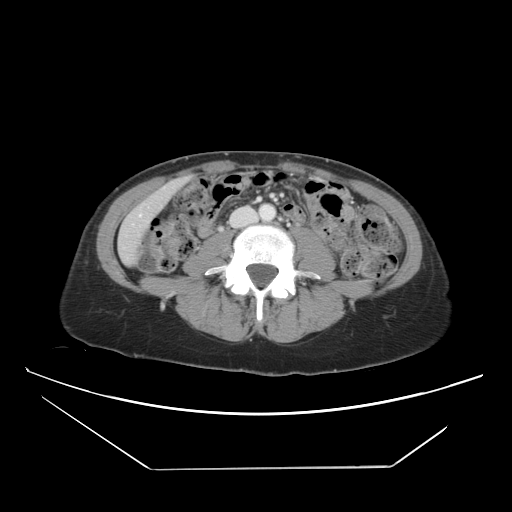
Contrast-enhanced abdominal CT, one axial slice. Position 8 of 42 along the scan axis. 120 kVp. Intravenous contrast given. Soft-tissue window (W 400 / L 40 HU). 5 mm slice thickness. 512 × 512 image matrix, field of view 399 × 399 mm. Female patient, age 52 years. Case-level facts recorded for this patient, not image findings: diagnosis: colorectal cancer liver metastases, imaged before liver resection; multiple liver metastases: yes; largest metastasis: 5.5 cm; disease in both lobes: yes.
Annotated regions visible in this slice (outlined manually by an expert reader):
- hepatic veins: bounding box [x1, y1, x2, y2] px = [131, 187, 166, 226]
- liver: [120, 182, 180, 264]
- planned liver remnant (the part of the liver to remain after resection): [130, 182, 181, 223]
- portal vein (with intrahepatic branches): [257, 198, 261, 201]